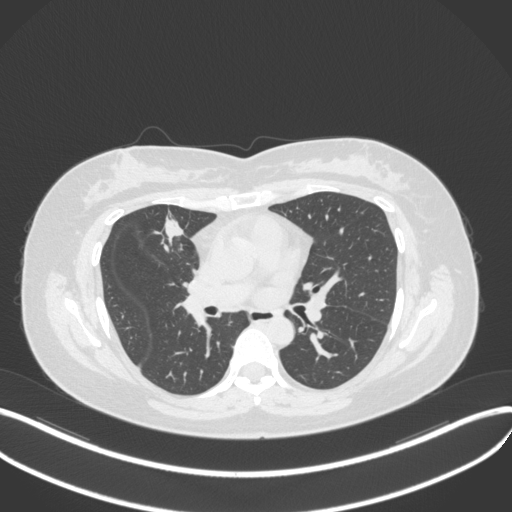
Chest CT, one axial slice. Slice 171 of 272 in the series (ordered by position). Reconstruction kernel B31f. 120 kVp. Lung window (W 1500 / L -600 HU). 1 mm slice thickness. 512 × 512 image matrix. Patient: female, 42 years. Case-level facts recorded for this patient, not image findings: clinical TNM (as recorded): T1b N0 M0.
Outlined on this slice (bounding box drawn by a radiologist):
- lung tumour (recorded histology: adenocarcinoma): bounding box <154,212,190,250> (left, top, right, bottom; pixels)